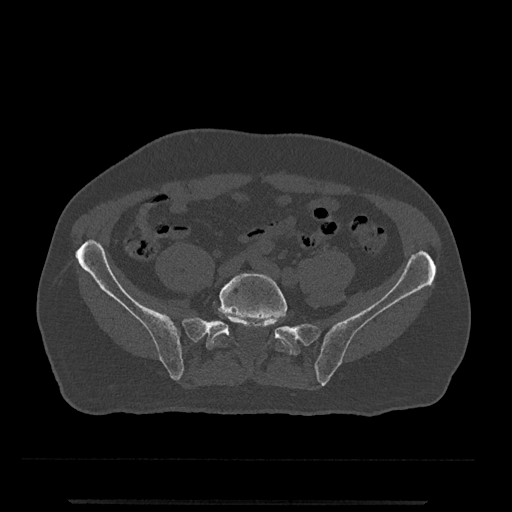
CT including the spine, one axial slice. Slice 45 of 797 in the series (ordered by position). Reconstruction kernel Br40s/3. 120 kVp. Bone window (W 1800 / L 400 HU). 0.5 mm slice thickness. 512 × 512 image matrix, field of view 419 × 419 mm. Patient: male, 63 years. Case-level facts recorded for this patient, not image findings: primary cancer: prostate.
Outlined on this slice (semi-automatically segmented with operator editing):
- L5 vertebra: bounding box [x1, y1, x2, y2] px = [209, 273, 291, 354]